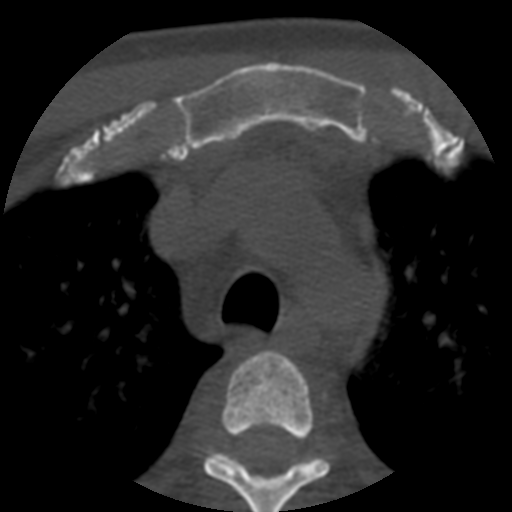
CT including the spine, one axial slice. Slice 411 of 508 in the series (ordered by position). Reconstruction kernel STANDARD. 120 kVp. Bone window (W 1800 / L 400 HU). 1.25 mm slice thickness. 512 × 512 image matrix, field of view 160 × 160 mm. Patient age 57 years. Case-level facts recorded for this patient, not image findings: primary cancer: prostate.
Structures marked on this image (semi-automatic segmentation, software-assisted and operator-edited):
- T3 vertebra: bounding box (x1, y1, x2, y2) in pixels: (203, 350, 331, 512)
- T4 vertebra: (224, 454, 319, 467)